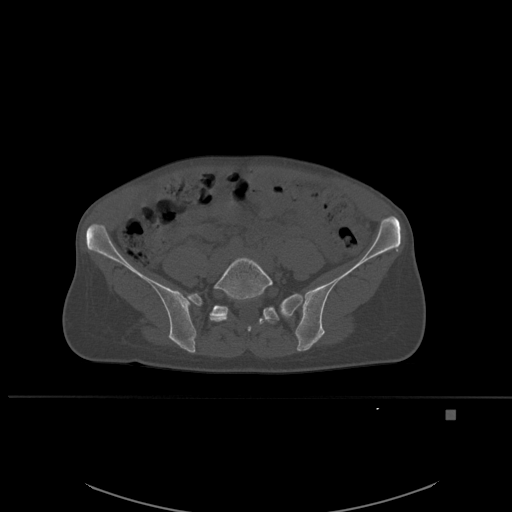
CT including the spine, one axial slice; position 167 of 537 along the scan axis; bone window (W 1800 / L 400 HU); 1.5 mm slice thickness; 512 × 512 image matrix. Female patient, age 45 years. Case-level facts recorded for this patient, not image findings: primary cancer: lung.
Outlined on this slice (semi-automatically segmented with operator editing):
- L5 vertebra: bounding box (x1, y1, x2, y2) in pixels: (209, 257, 273, 332)